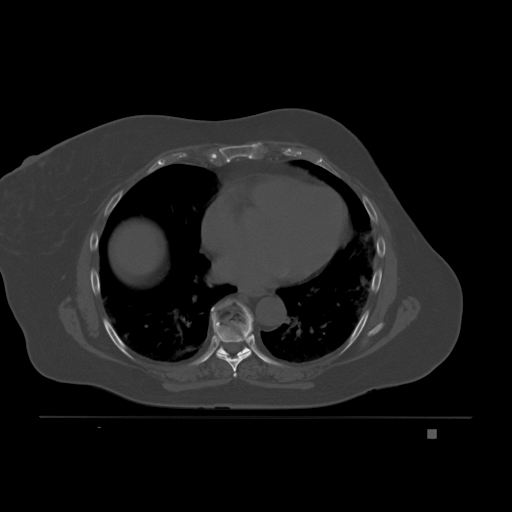
CT including the spine, one axial slice; bone window (W 1800 / L 400 HU); 3 mm slice thickness; 512 × 512 image matrix, field of view 474 × 474 mm. Patient: female, 63 years. Case-level facts recorded for this patient, not image findings: primary cancer: breast.
Structures marked on this image (semi-automatically segmented with operator editing):
- T7 vertebra: bounding box (x1, y1, x2, y2) in pixels: (216, 339, 252, 377)
- T8 vertebra: (211, 300, 253, 355)